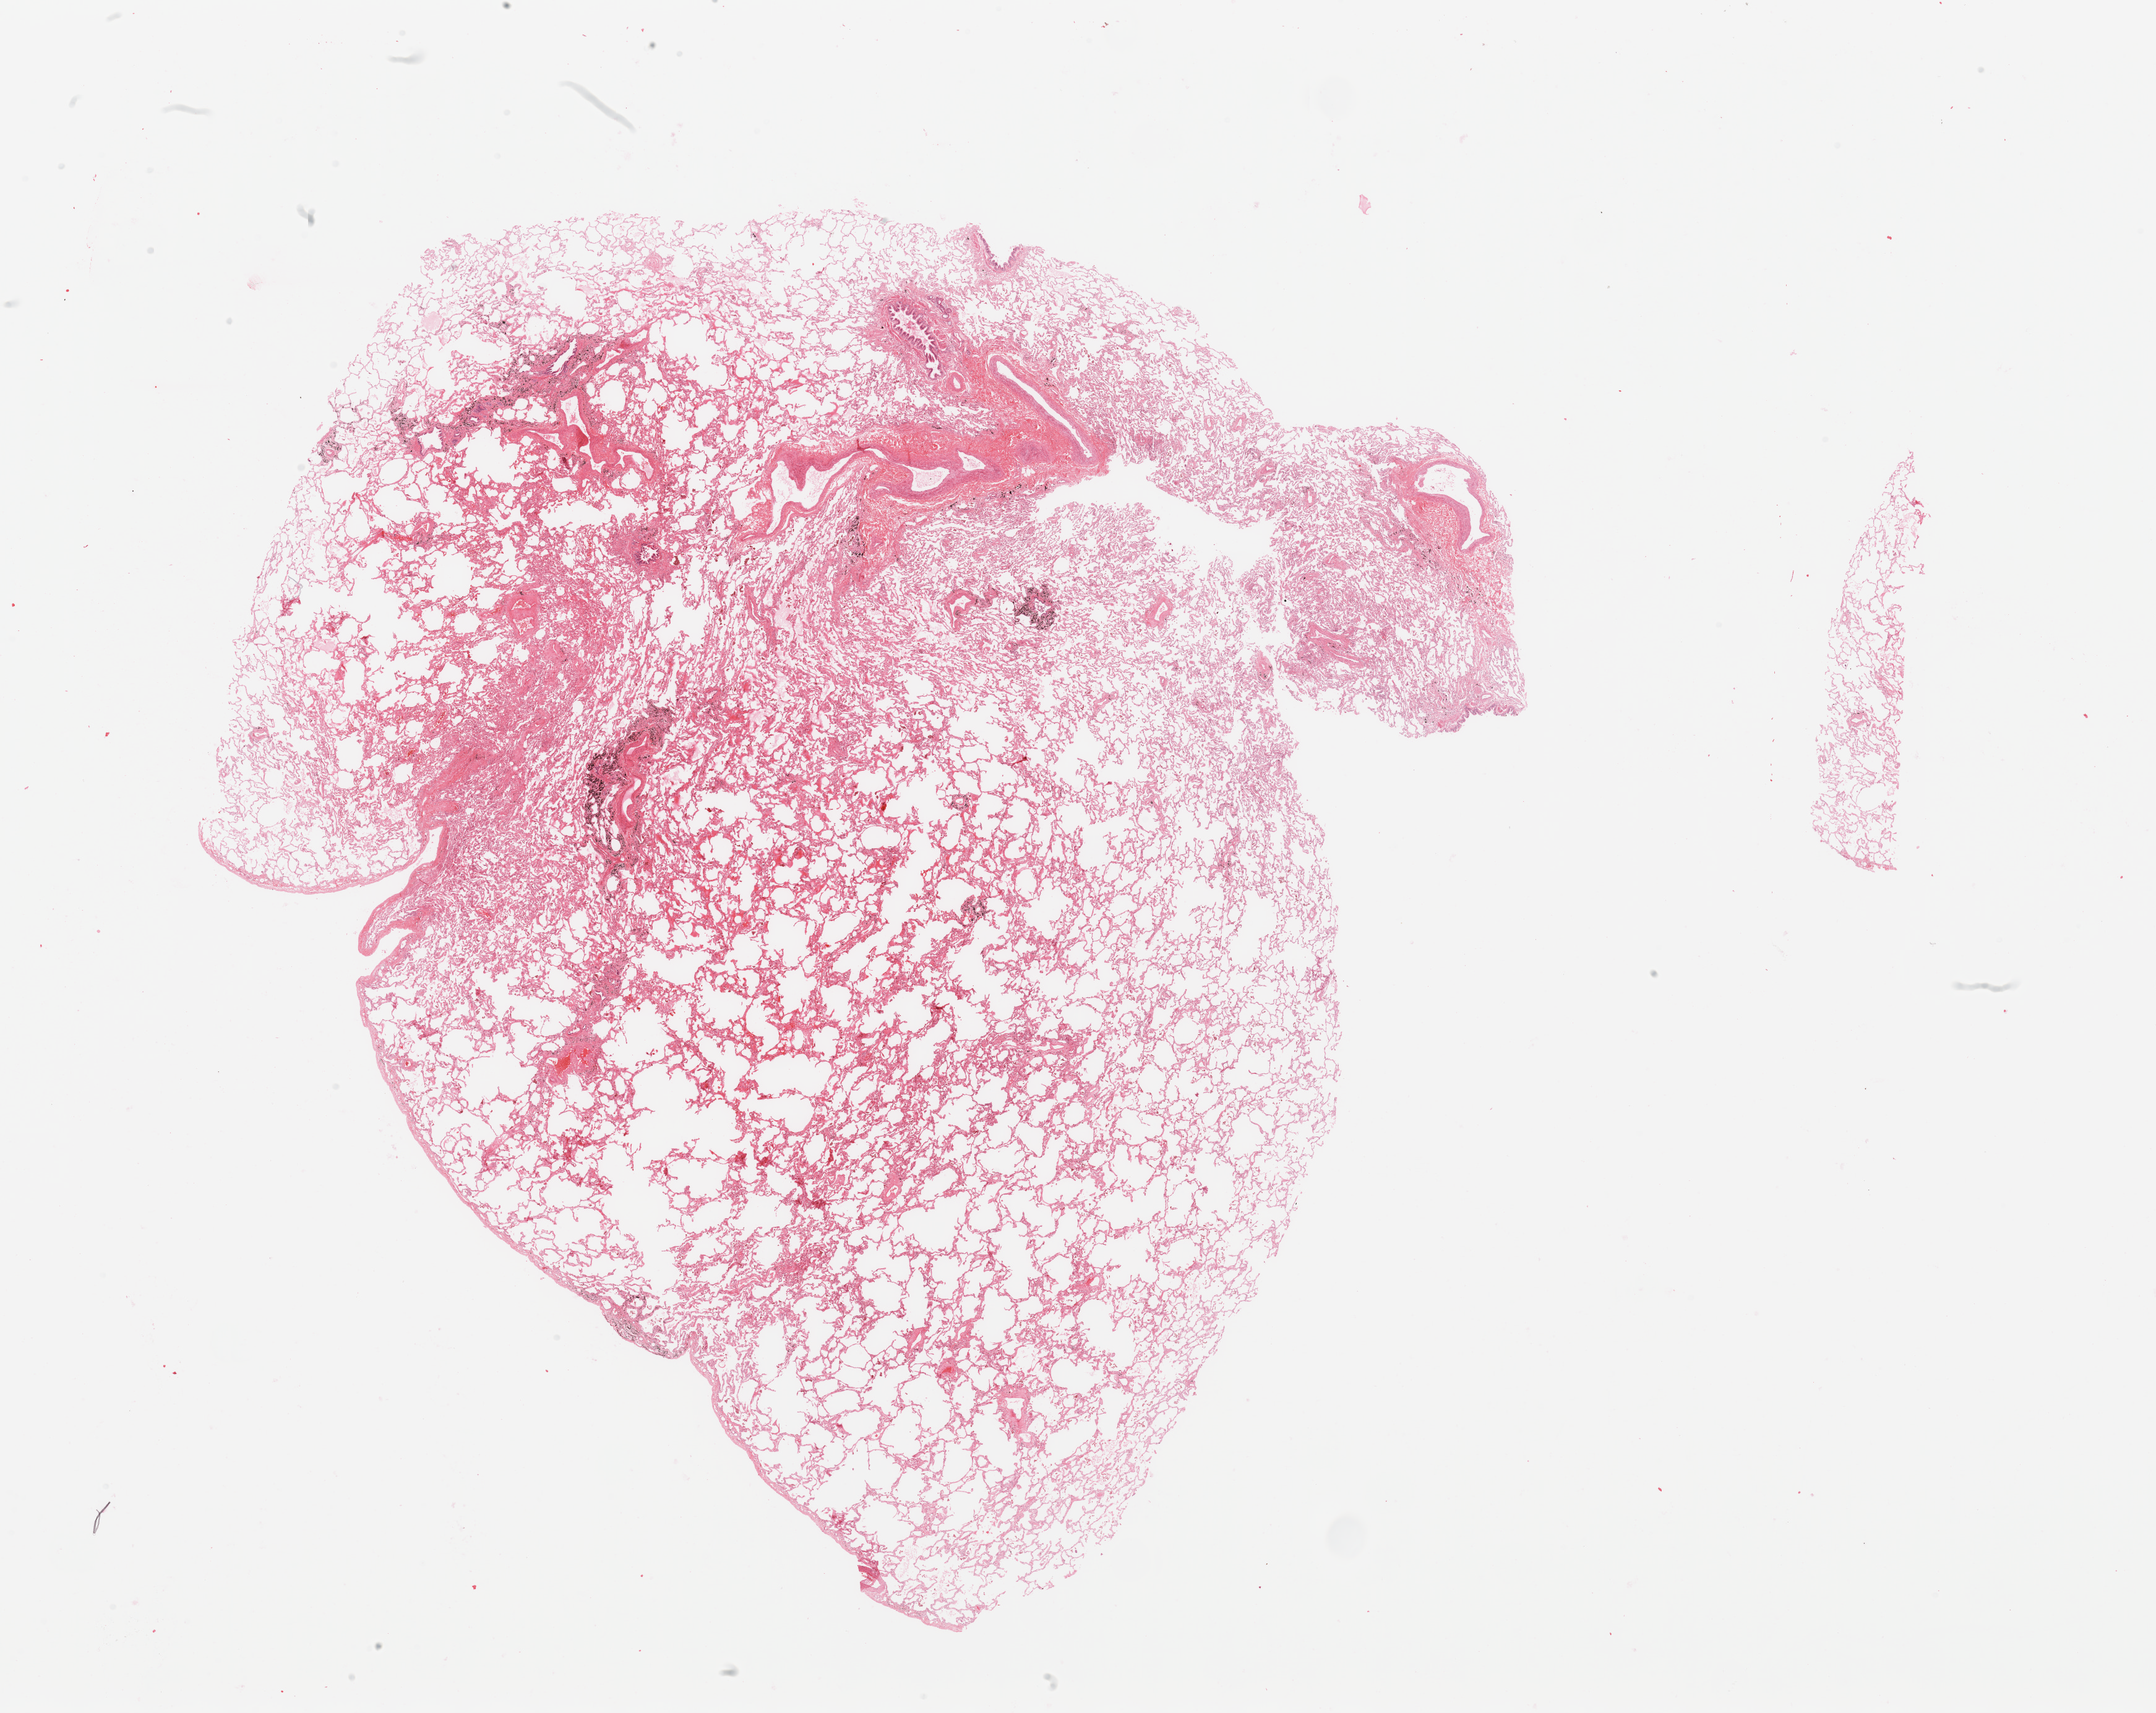
H&E-stained whole-slide image, low-resolution overview of the scanned area, about 27.6 x 21.9 mm; normal (non-tumour) tissue sample, sampled site: lung. Female, 67 y/o.
- this section: normal (non-tumour) tissue from the same patient
- patient diagnosis: Adenocarcinoma, NOS